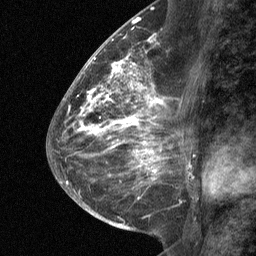
Breast MRI (dynamic contrast-enhanced), one sagittal slice; slice 33 of 64 in the series (ordered by position); dynamic contrast-enhanced study with each time point stored as its own series, time point 2 of 3 at this slice position (early post-contrast, ordered by acquisition time); 1.5 T; TE 4.8 ms, TR 27 ms; 2 mm slice thickness; 256 × 256 image matrix, field of view 180 × 180 mm. Patient: female, 59 years. Case-level facts recorded for this patient, not image findings: setting: breast cancer imaged before/during neoadjuvant chemotherapy; receptor status: triple-negative.
Annotated regions visible in this slice (semi-automatically segmented with operator editing):
- analysis volume of interest (the breast-tissue region the enhancement analysis was run in; not a lesion): box from (x=122, y=58) to (x=170, y=109) px
- tumour enhancement mask (voxels above the 90 % enhancement threshold inside the analysis volume of interest): (x=122, y=58)–(x=164, y=109)